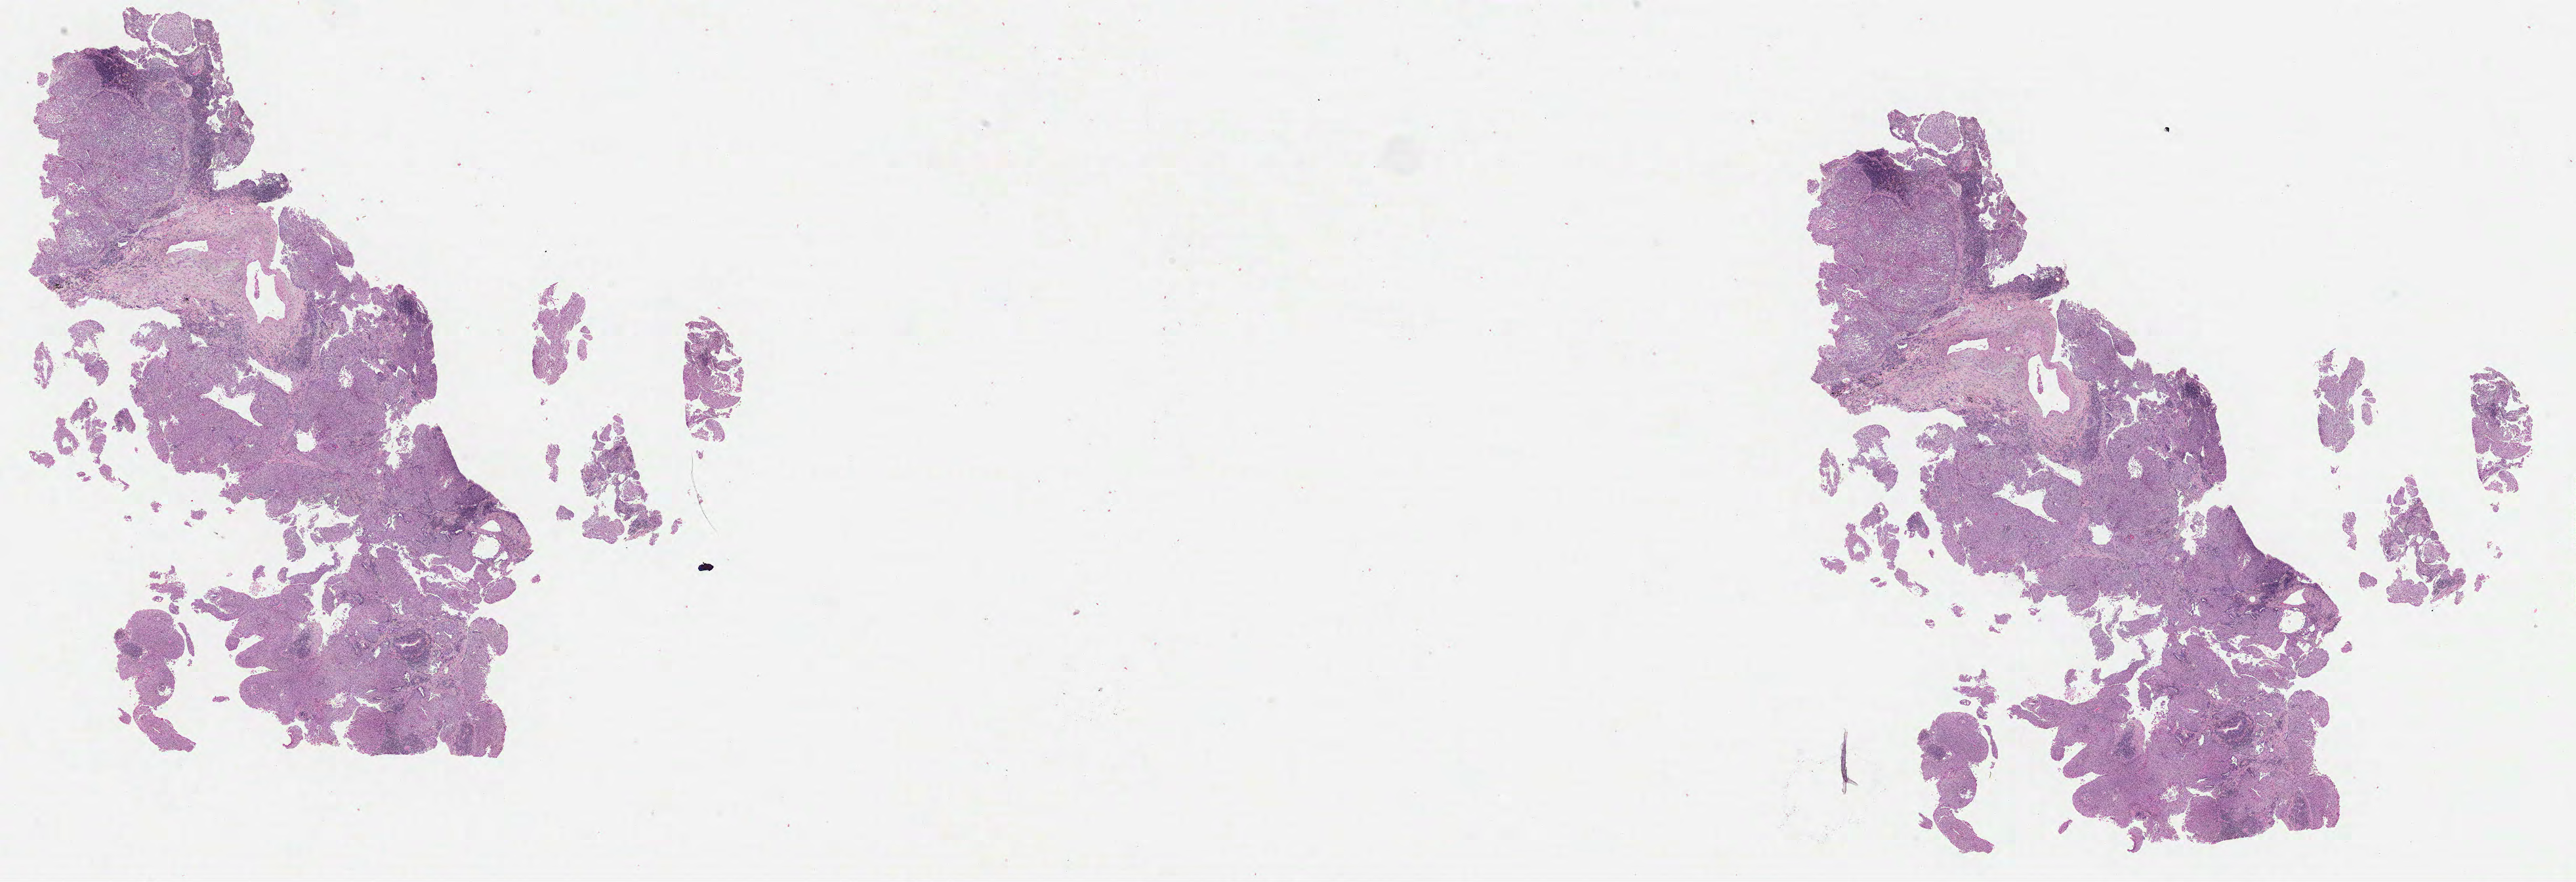
Hematoxylin and eosin (H&E) stained whole-slide image — whole scanned area (about 31.7 x 10.8 mm, acquisition: 40x scan) shown as a low-resolution overview. Formalin-fixed paraffin-embedded (FFPE) diagnostic section. Lung, primary tumour sample. Patient: male, age at initial diagnosis 67 years.
- AJCC pathologic stage: IIIB (6th edition)
- pathologic diagnosis: Squamous cell carcinoma, NOS (lower lobe, lung)